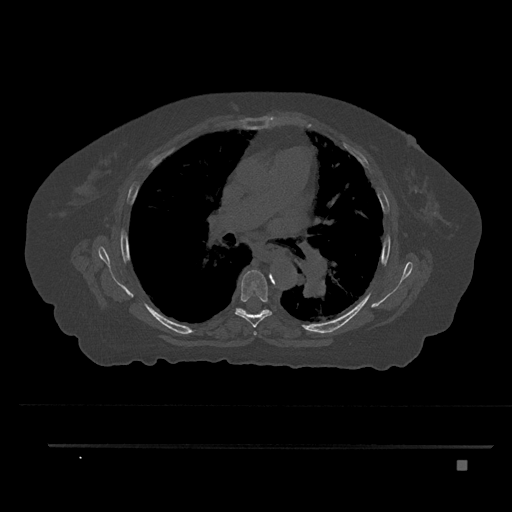
CT including the spine, one axial slice; slice 524 of 797 in the series (ordered by position); reconstruction kernel Br40s/3; 120 kVp; bone window (W 1800 / L 400 HU); 0.5 mm slice thickness; 512 × 512 image matrix. Patient: female, 76 years. Case-level facts recorded for this patient, not image findings: primary cancer: lung.
Outlined on this slice (semi-automatic segmentation, software-assisted and operator-edited):
- T5 vertebra: bounding box <253,331,257,335> (left, top, right, bottom; pixels)
- T6 vertebra: <235,270,272,328>
- T7 vertebra: <236,308,268,313>